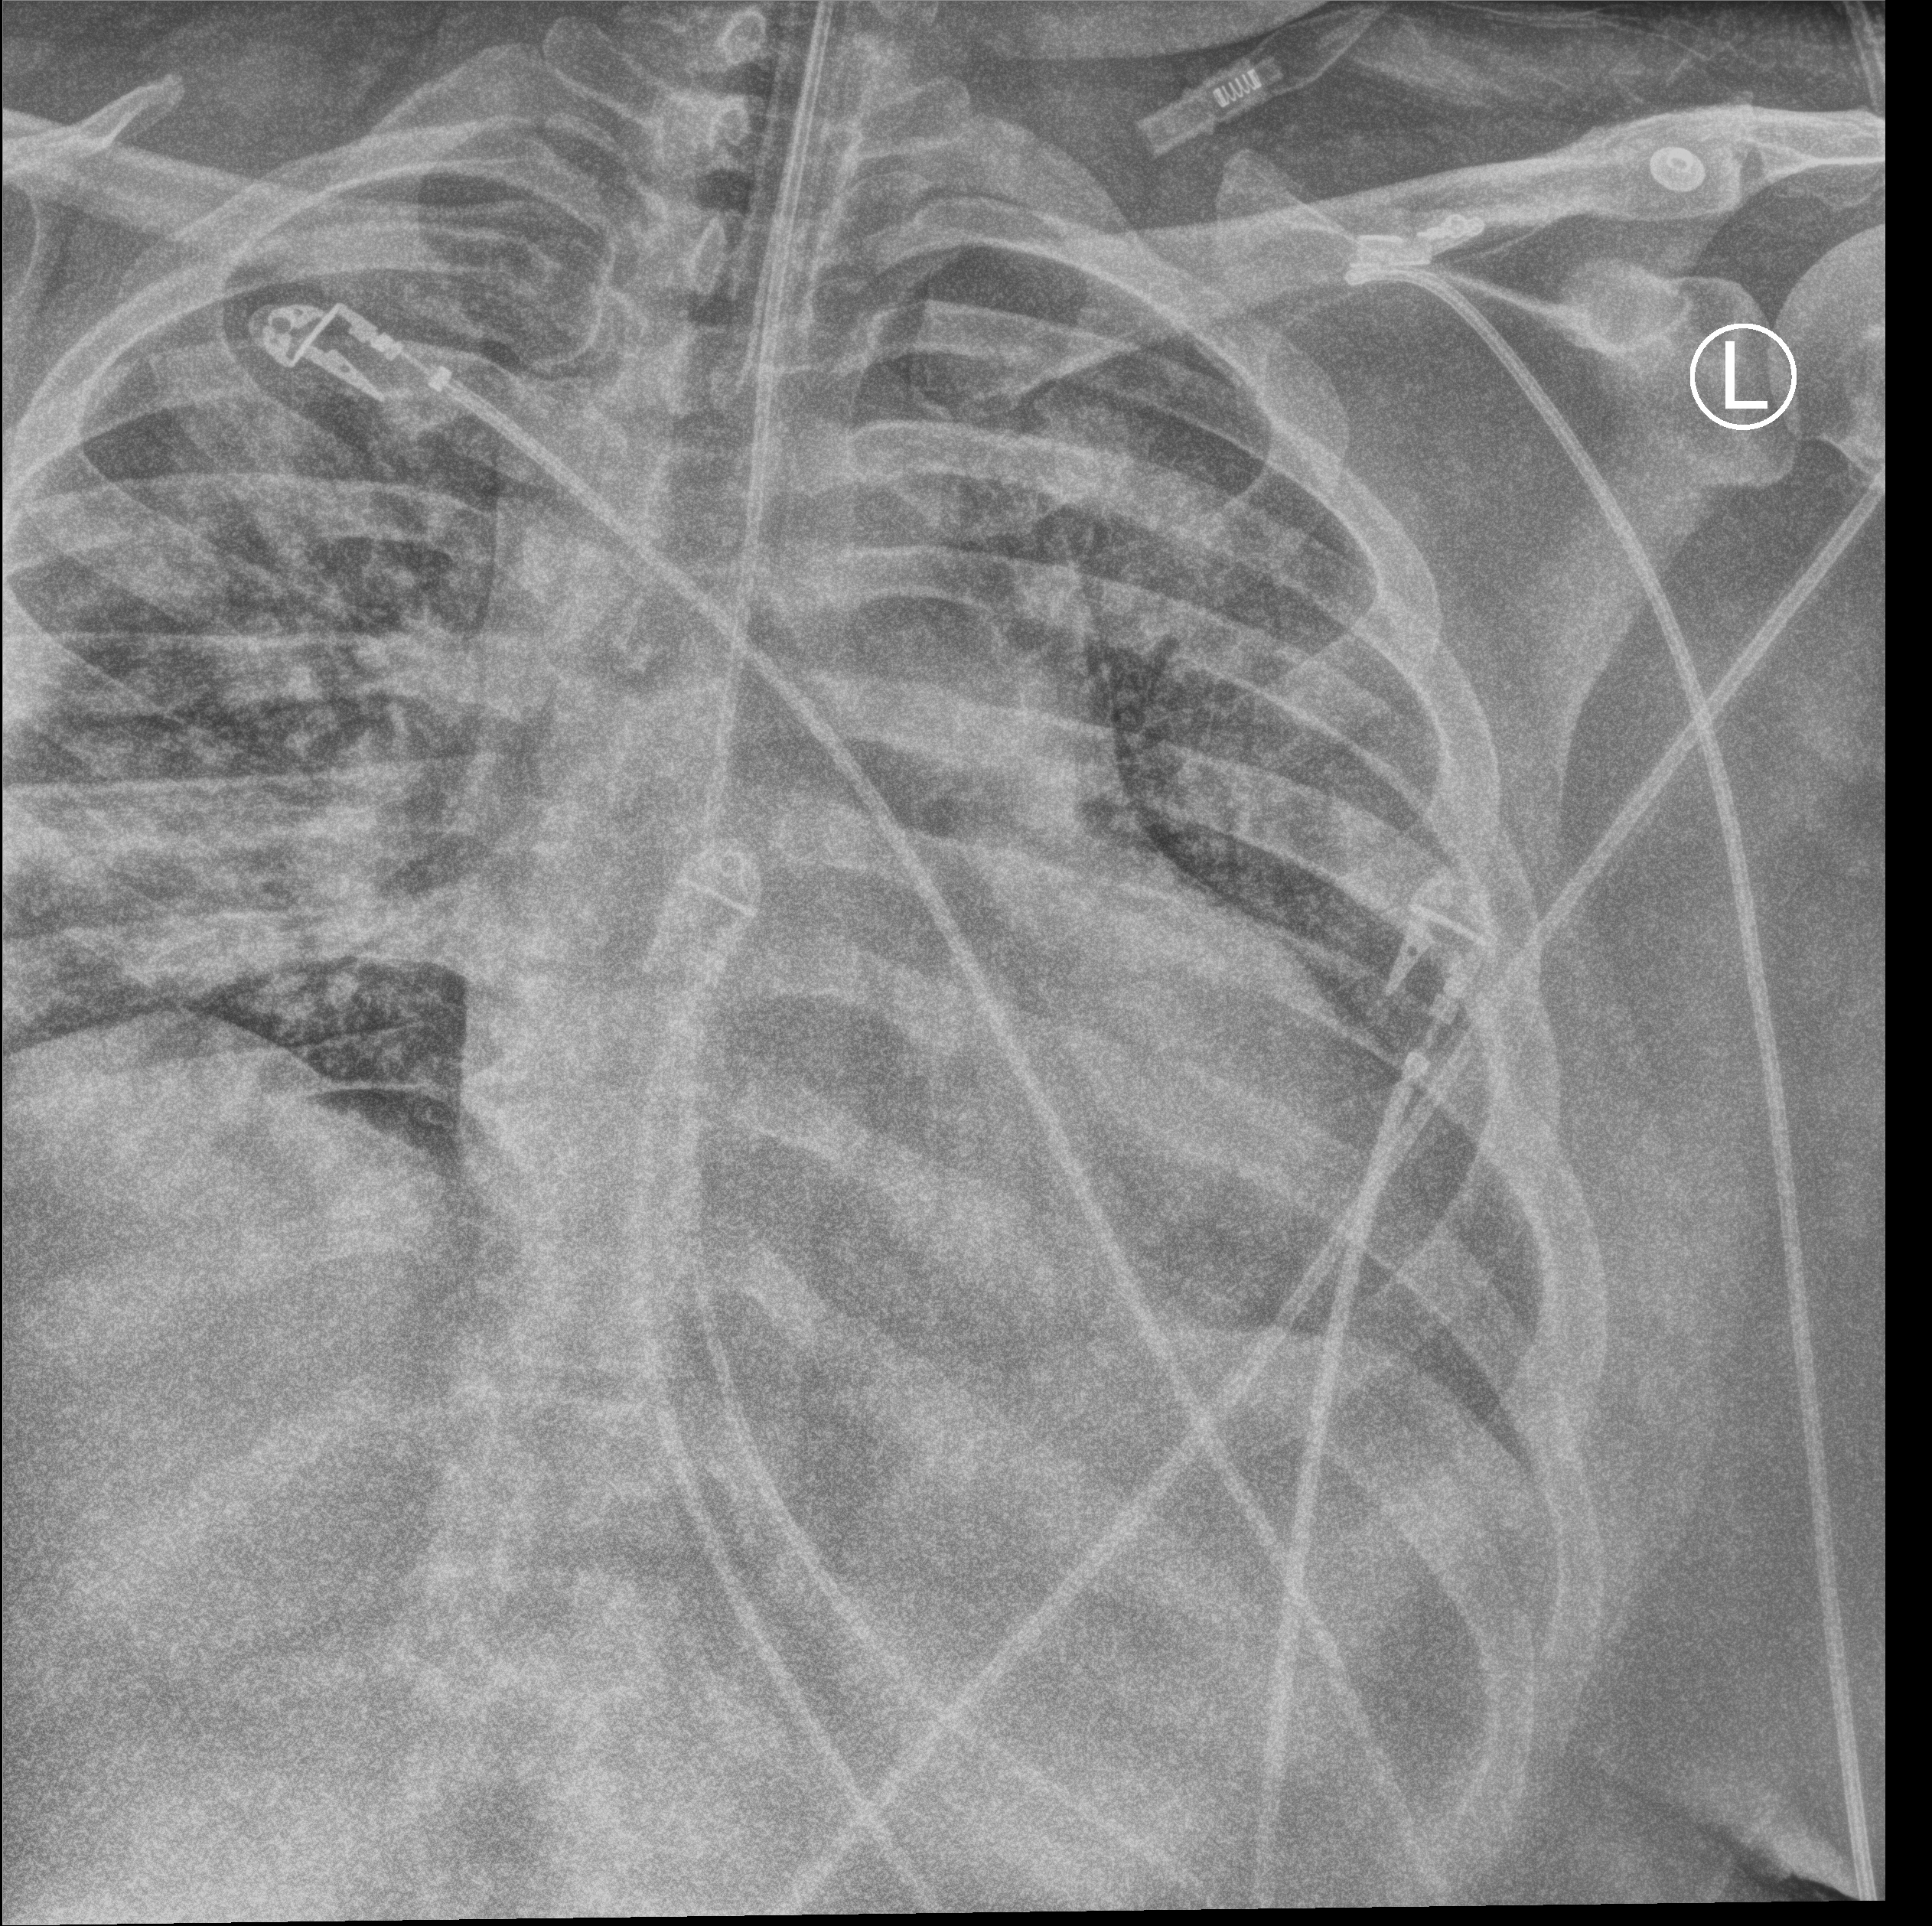
Bedside chest radiograph (computed radiography); anteroposterior (AP) projection. Patient hospitalised with COVID-19, aged 18–59 years.
Hospital-stay facts (about this admission, not read from this image; timing relative to this image not recorded):
- length of hospital stay: 10 days
- diabetes (admission record): yes